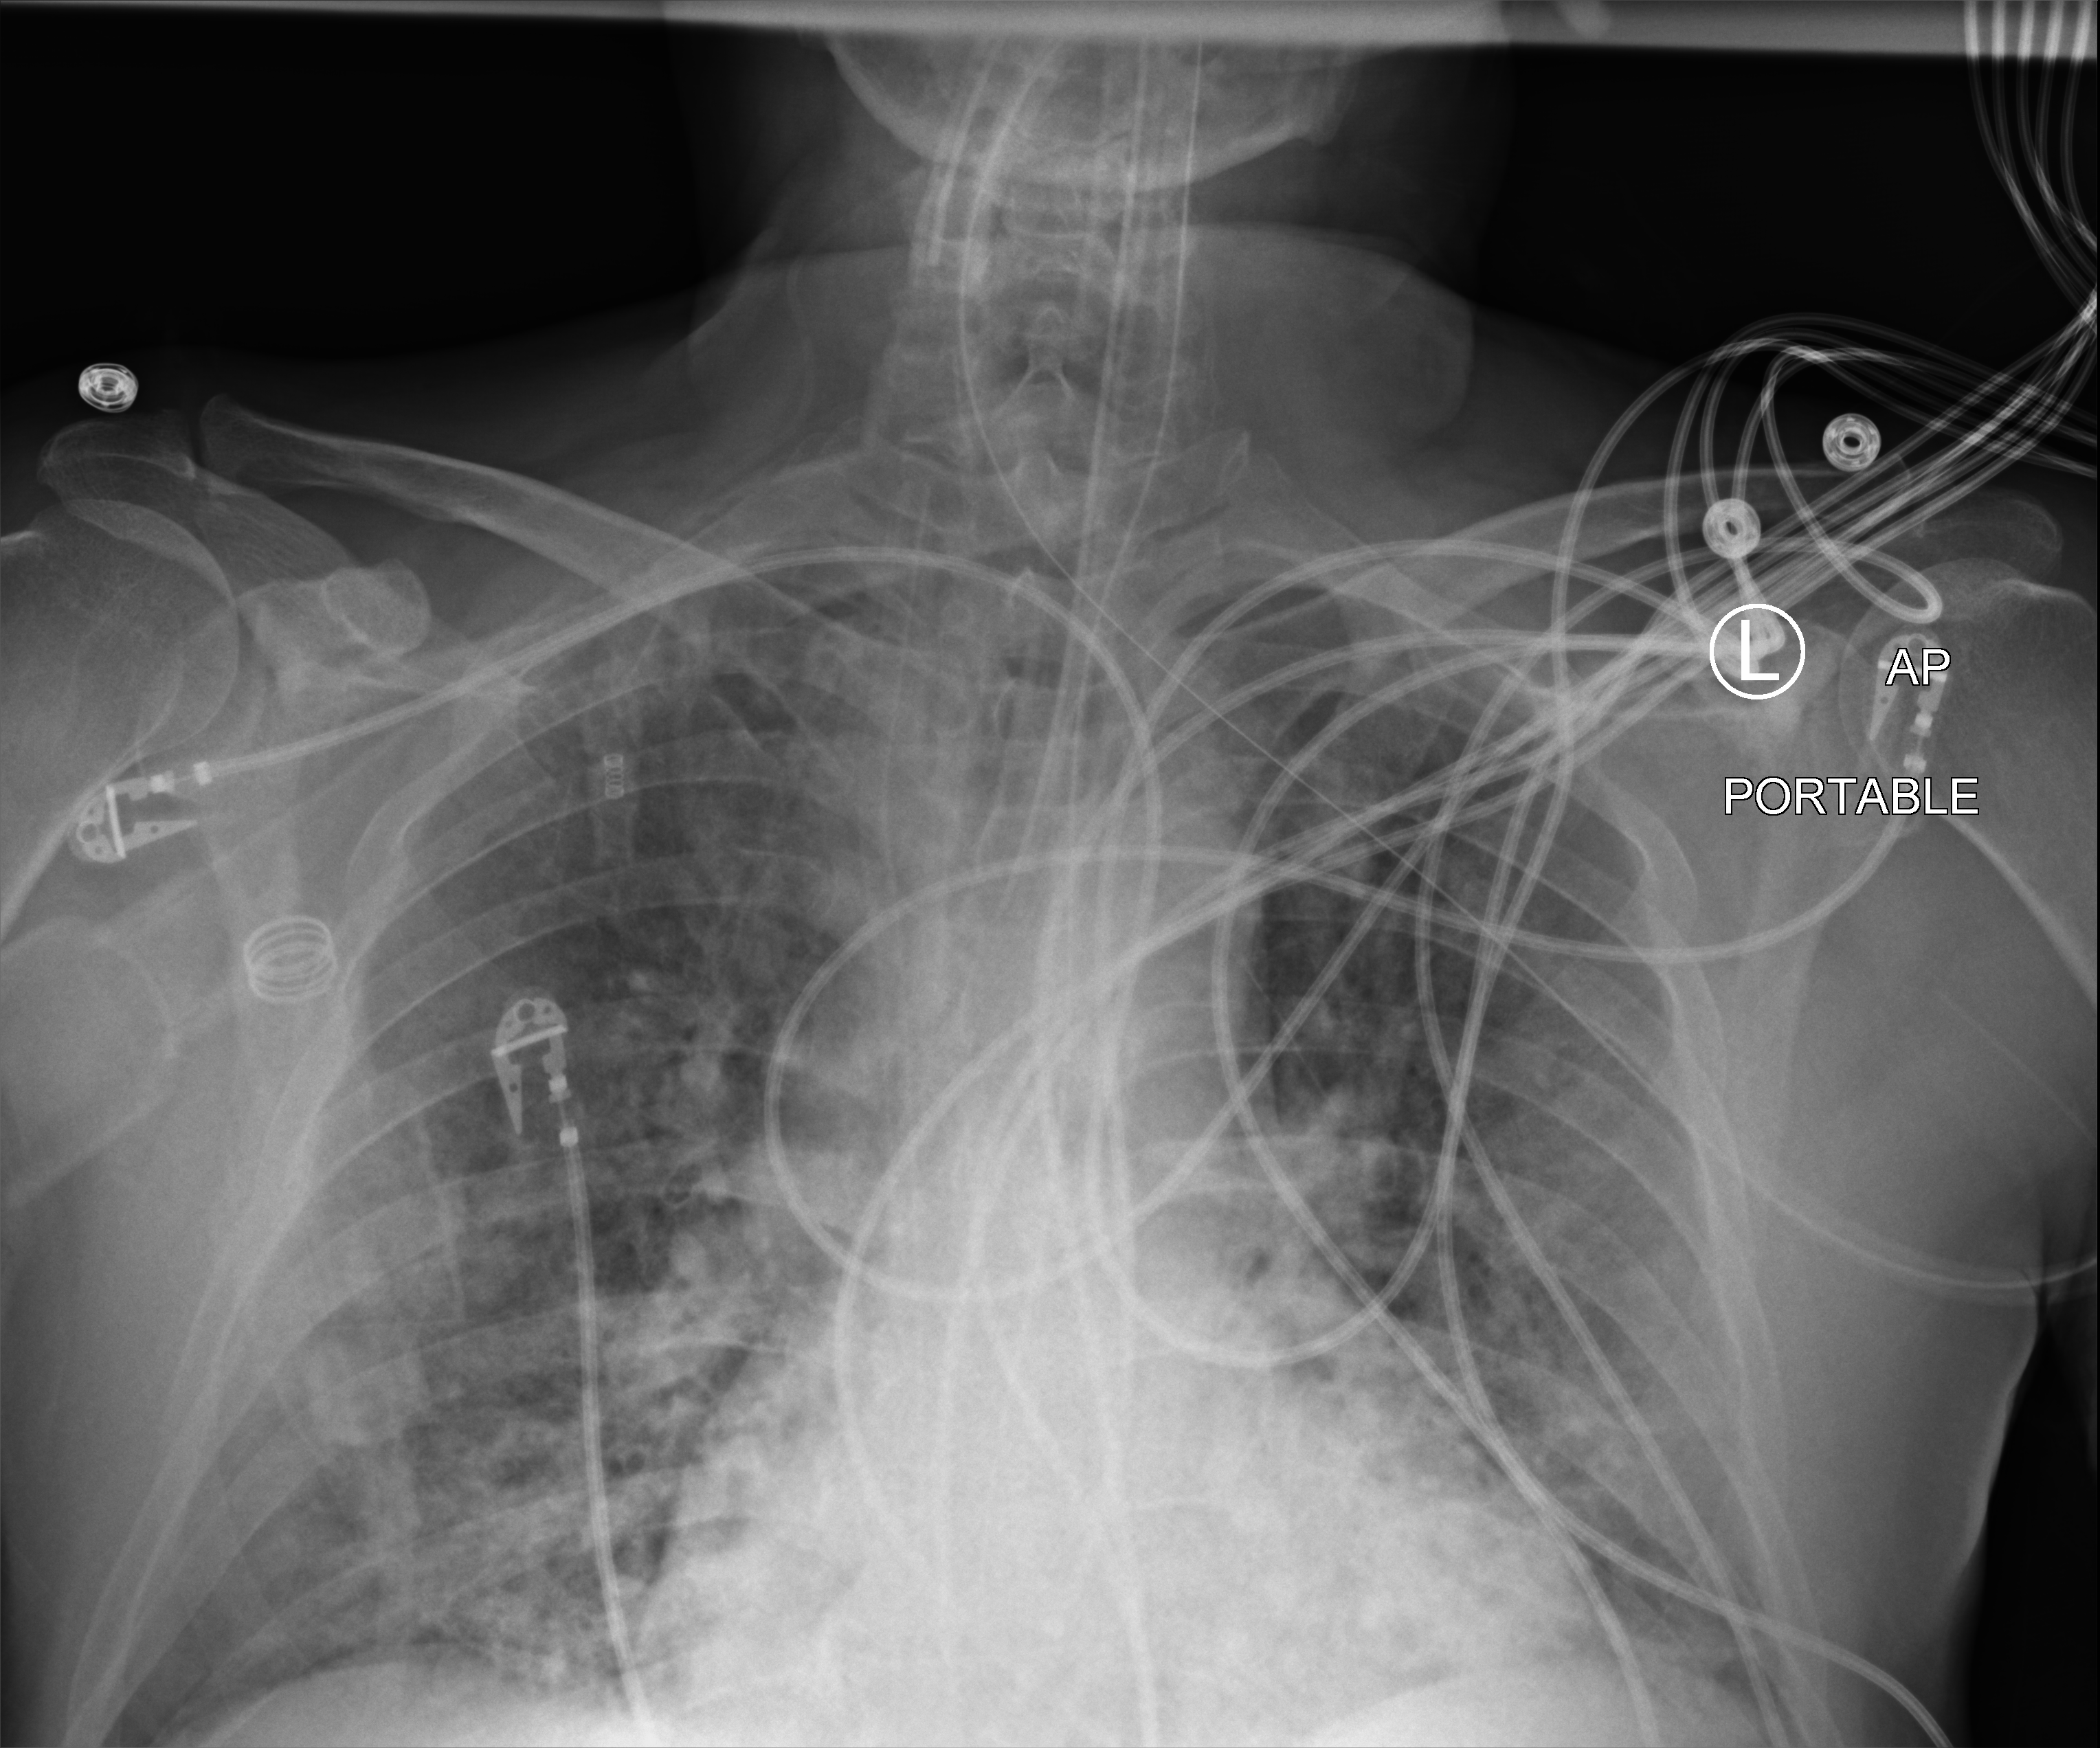
Portable chest radiograph. Male patient hospitalised with COVID-19, age 18–59 years.
From the hospital-stay record, not from the radiograph (when in the stay this image was taken is not recorded):
- admitted to intensive care during this hospital stay: no
- length of hospital stay: 19 days